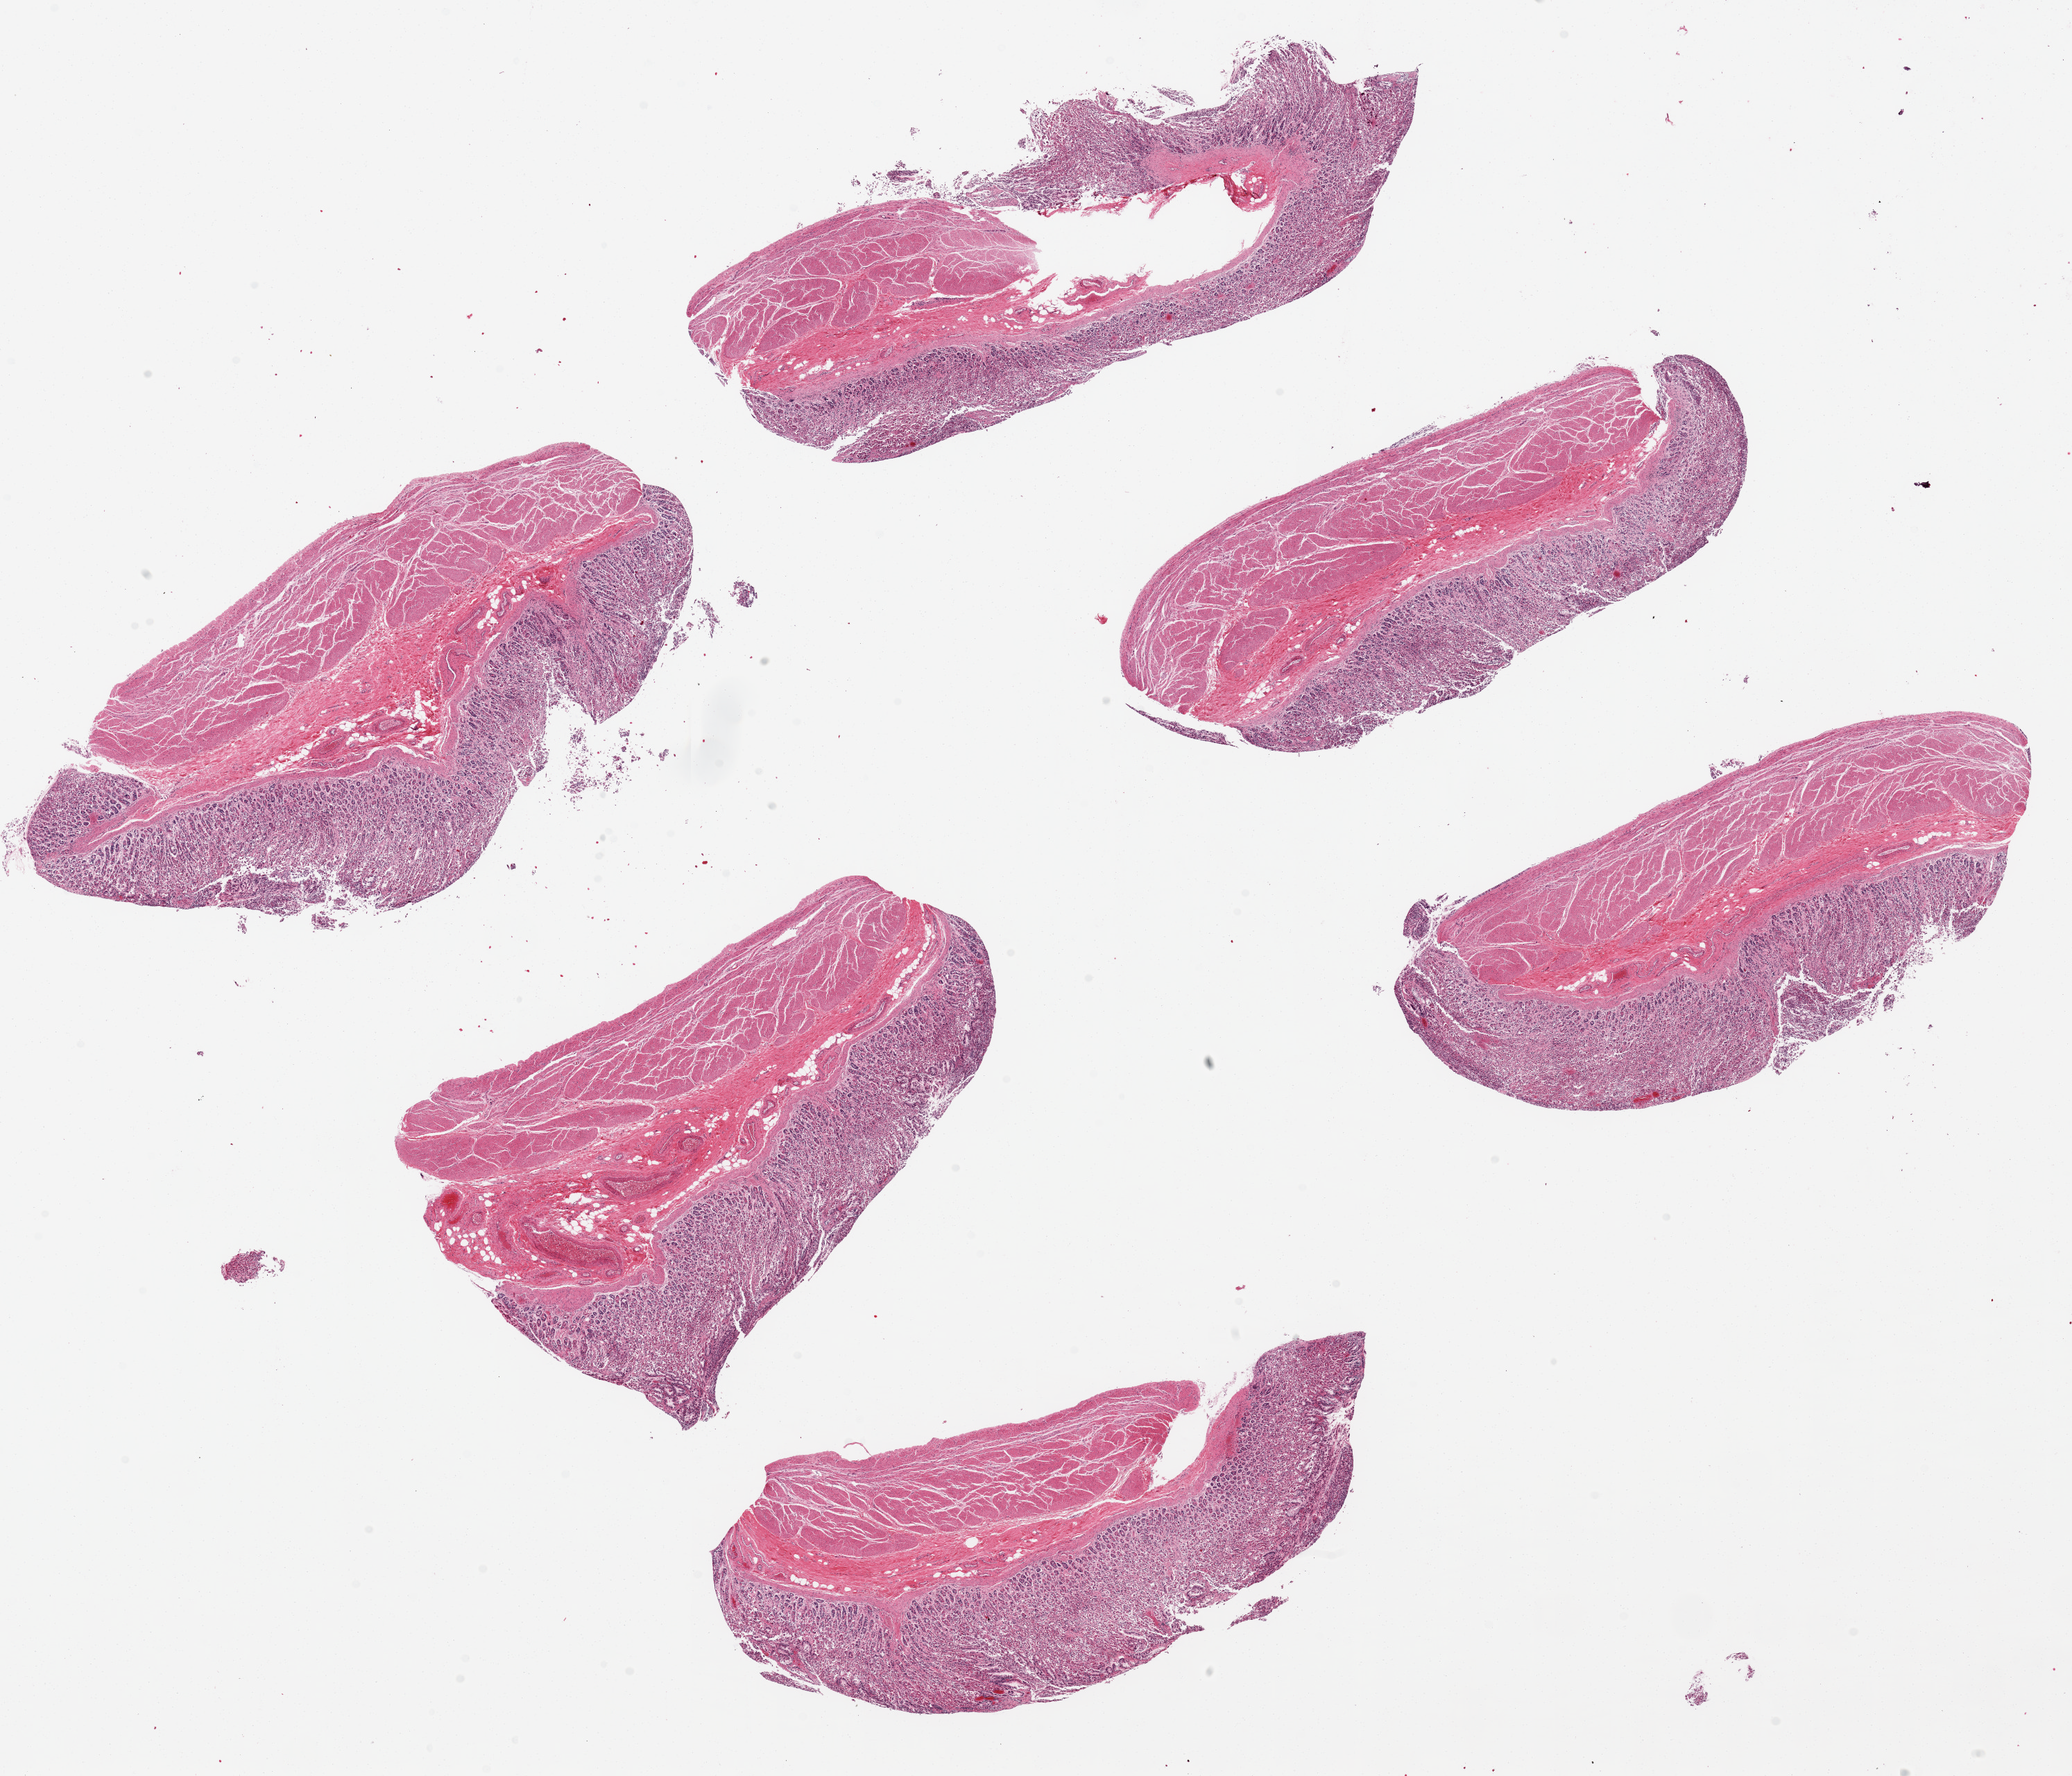
Digitized H&E-stained section, shown as a low-resolution overview of the whole scanned area (about 23.6 x 20.2 mm, slide scanned at 20x), PAXgene-fixed paraffin-embedded (PFPE) section, sampled site (target tissue): stomach, tissue donor sample. Donor sex: female.
* review note (as recorded): 6 ~7.5x3mm pieces. Autolyzed mucosa is ~3-45% of thickness